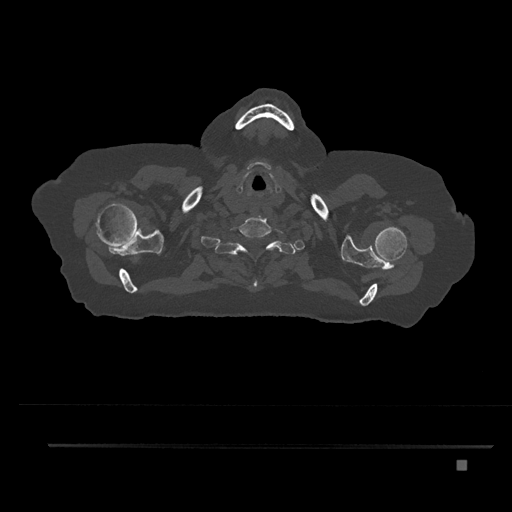
CT including the spine, one axial slice. Slice 710 of 797 in the series (ordered by position). Reconstruction kernel Br40s/3. 120 kVp. Bone window (W 1800 / L 400 HU). 0.5 mm slice thickness. 512 × 512 image matrix, field of view 437 × 437 mm. Patient: female, 76 years. Case-level facts recorded for this patient, not image findings: primary cancer: lung.
Outlined on this slice (semi-automatic segmentation, software-assisted and operator-edited):
- T1 vertebra: box from (x=223, y=237) to (x=285, y=287) px